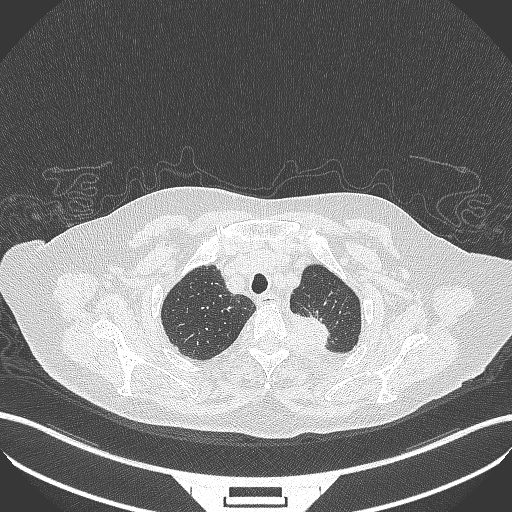
Chest CT, one axial slice. Position 299 of 353 along the scan axis. 100 kVp. Lung window (W 1500 / L -600 HU). 1 mm slice thickness. 512 × 512 image matrix, field of view 400 × 400 mm. Female patient, age 81 years. From the clinical record (not read from this slice): clinical TNM (as recorded): T2a N0 M0.
Structures marked on this image (bounding box drawn by a radiologist):
- lung tumour (recorded histology: adenocarcinoma): bounding box <282,306,335,352> (left, top, right, bottom; pixels)